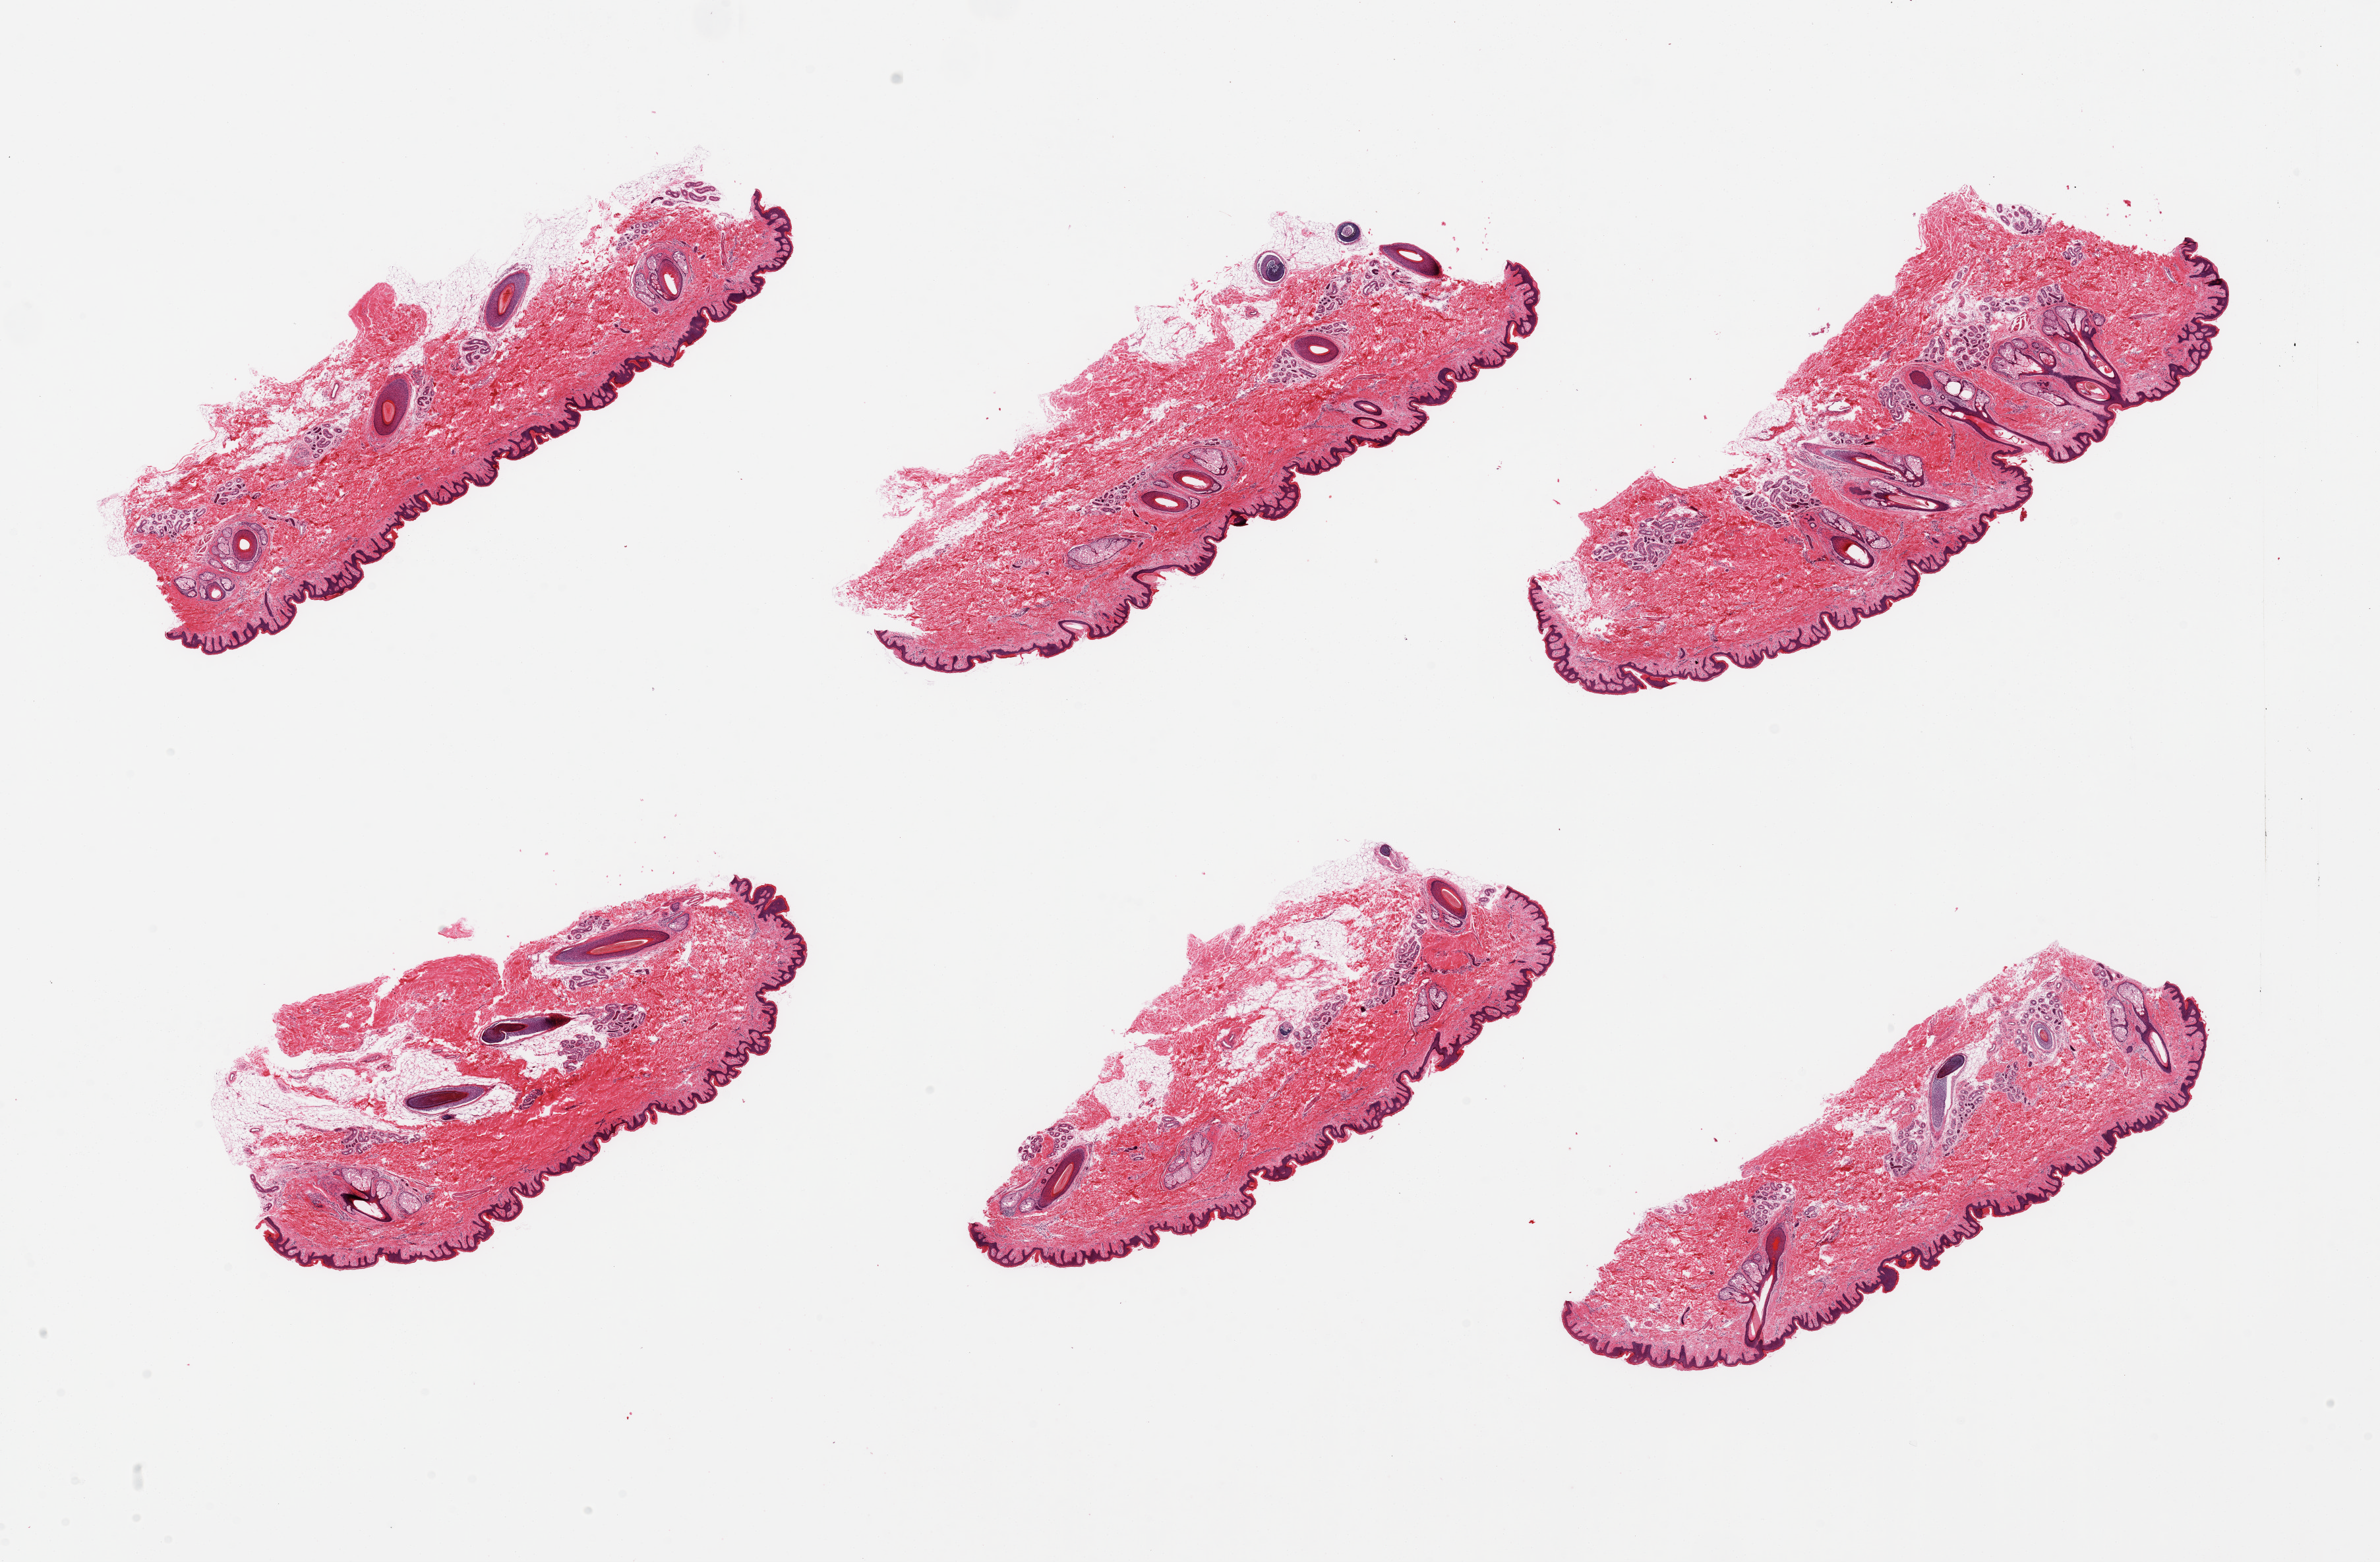
Whole-slide image, hematoxylin and eosin (H&E) stain, brightfield — a low-resolution overview of the entire scanned area, about 28.5 x 18.7 mm. PAXgene-fixed, paraffin-embedded tissue. Target tissue: skin of suprapubic region. Donor tissue sample. Male donor.
Pathologist's review note for this sample: 6 pieces, minimal dermal fat, squamous epithelium is 30-50 microns.